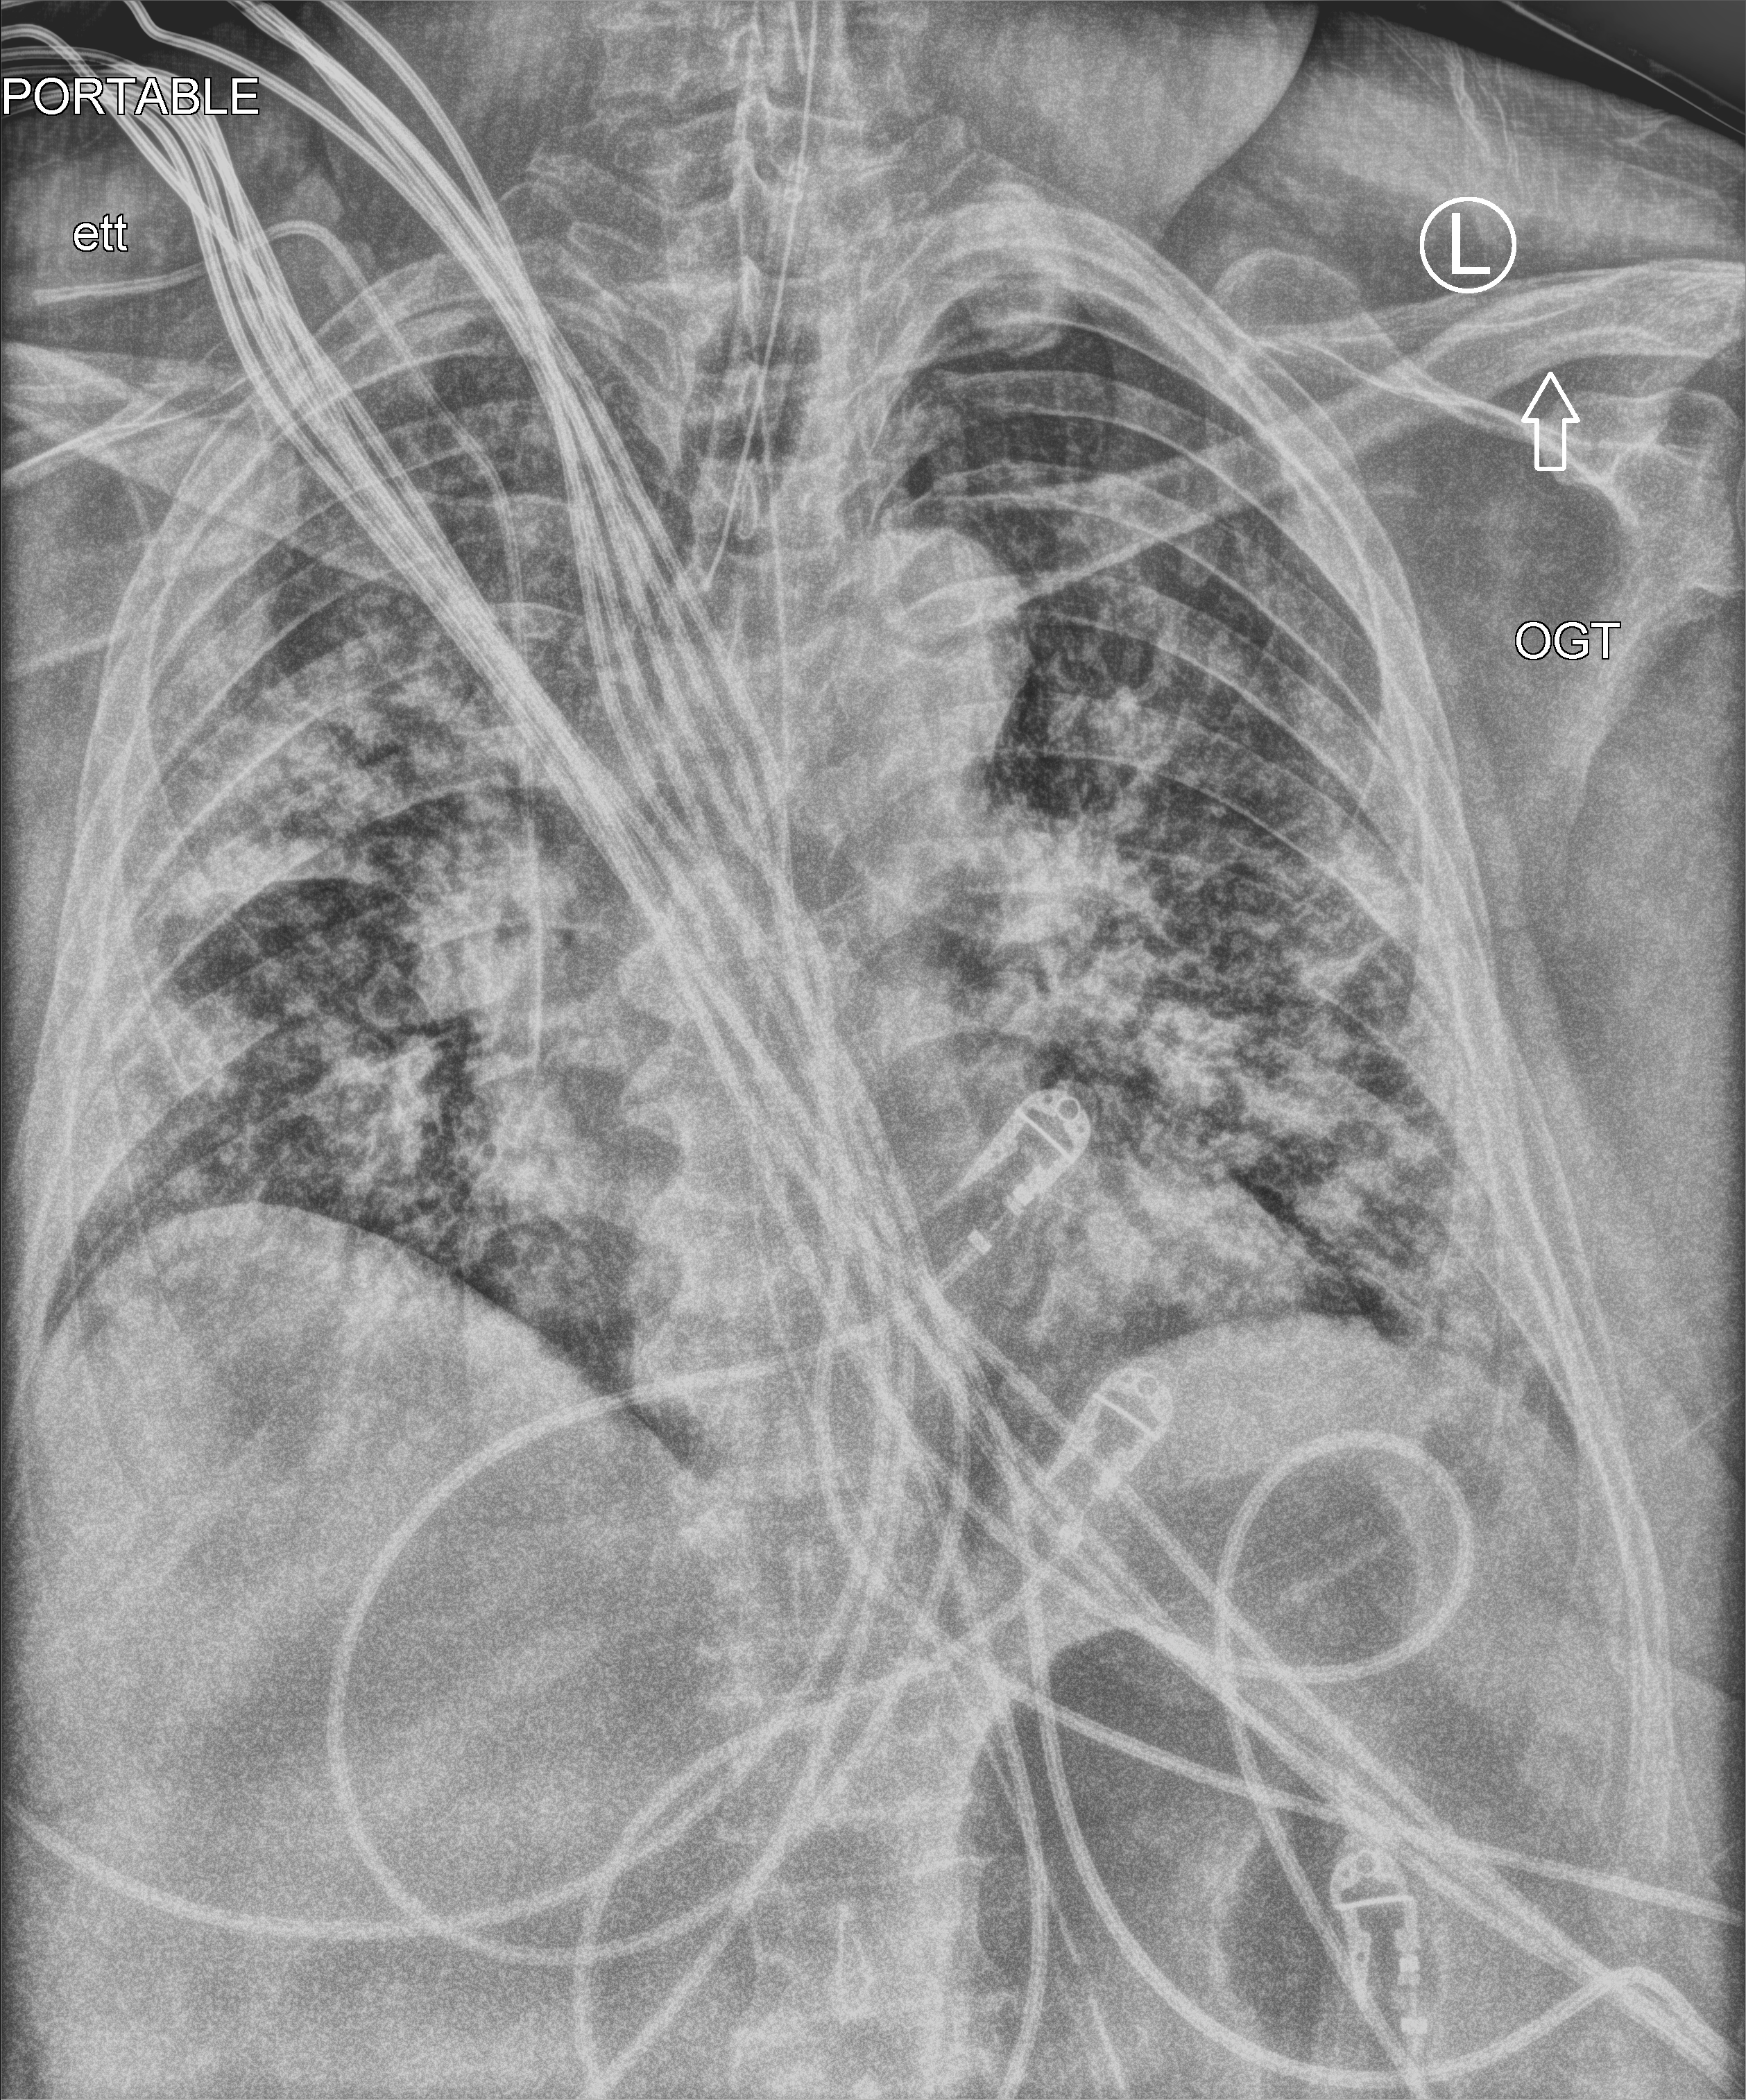
Portable chest radiograph, anteroposterior (AP) projection. Patient hospitalised with COVID-19, aged 18–59 years.
From the hospital-stay record, not from the radiograph (when in the stay this image was taken is not recorded): length of hospital stay: 28 days; admitted to intensive care during this hospital stay: yes; mechanically ventilated during this hospital stay: yes.